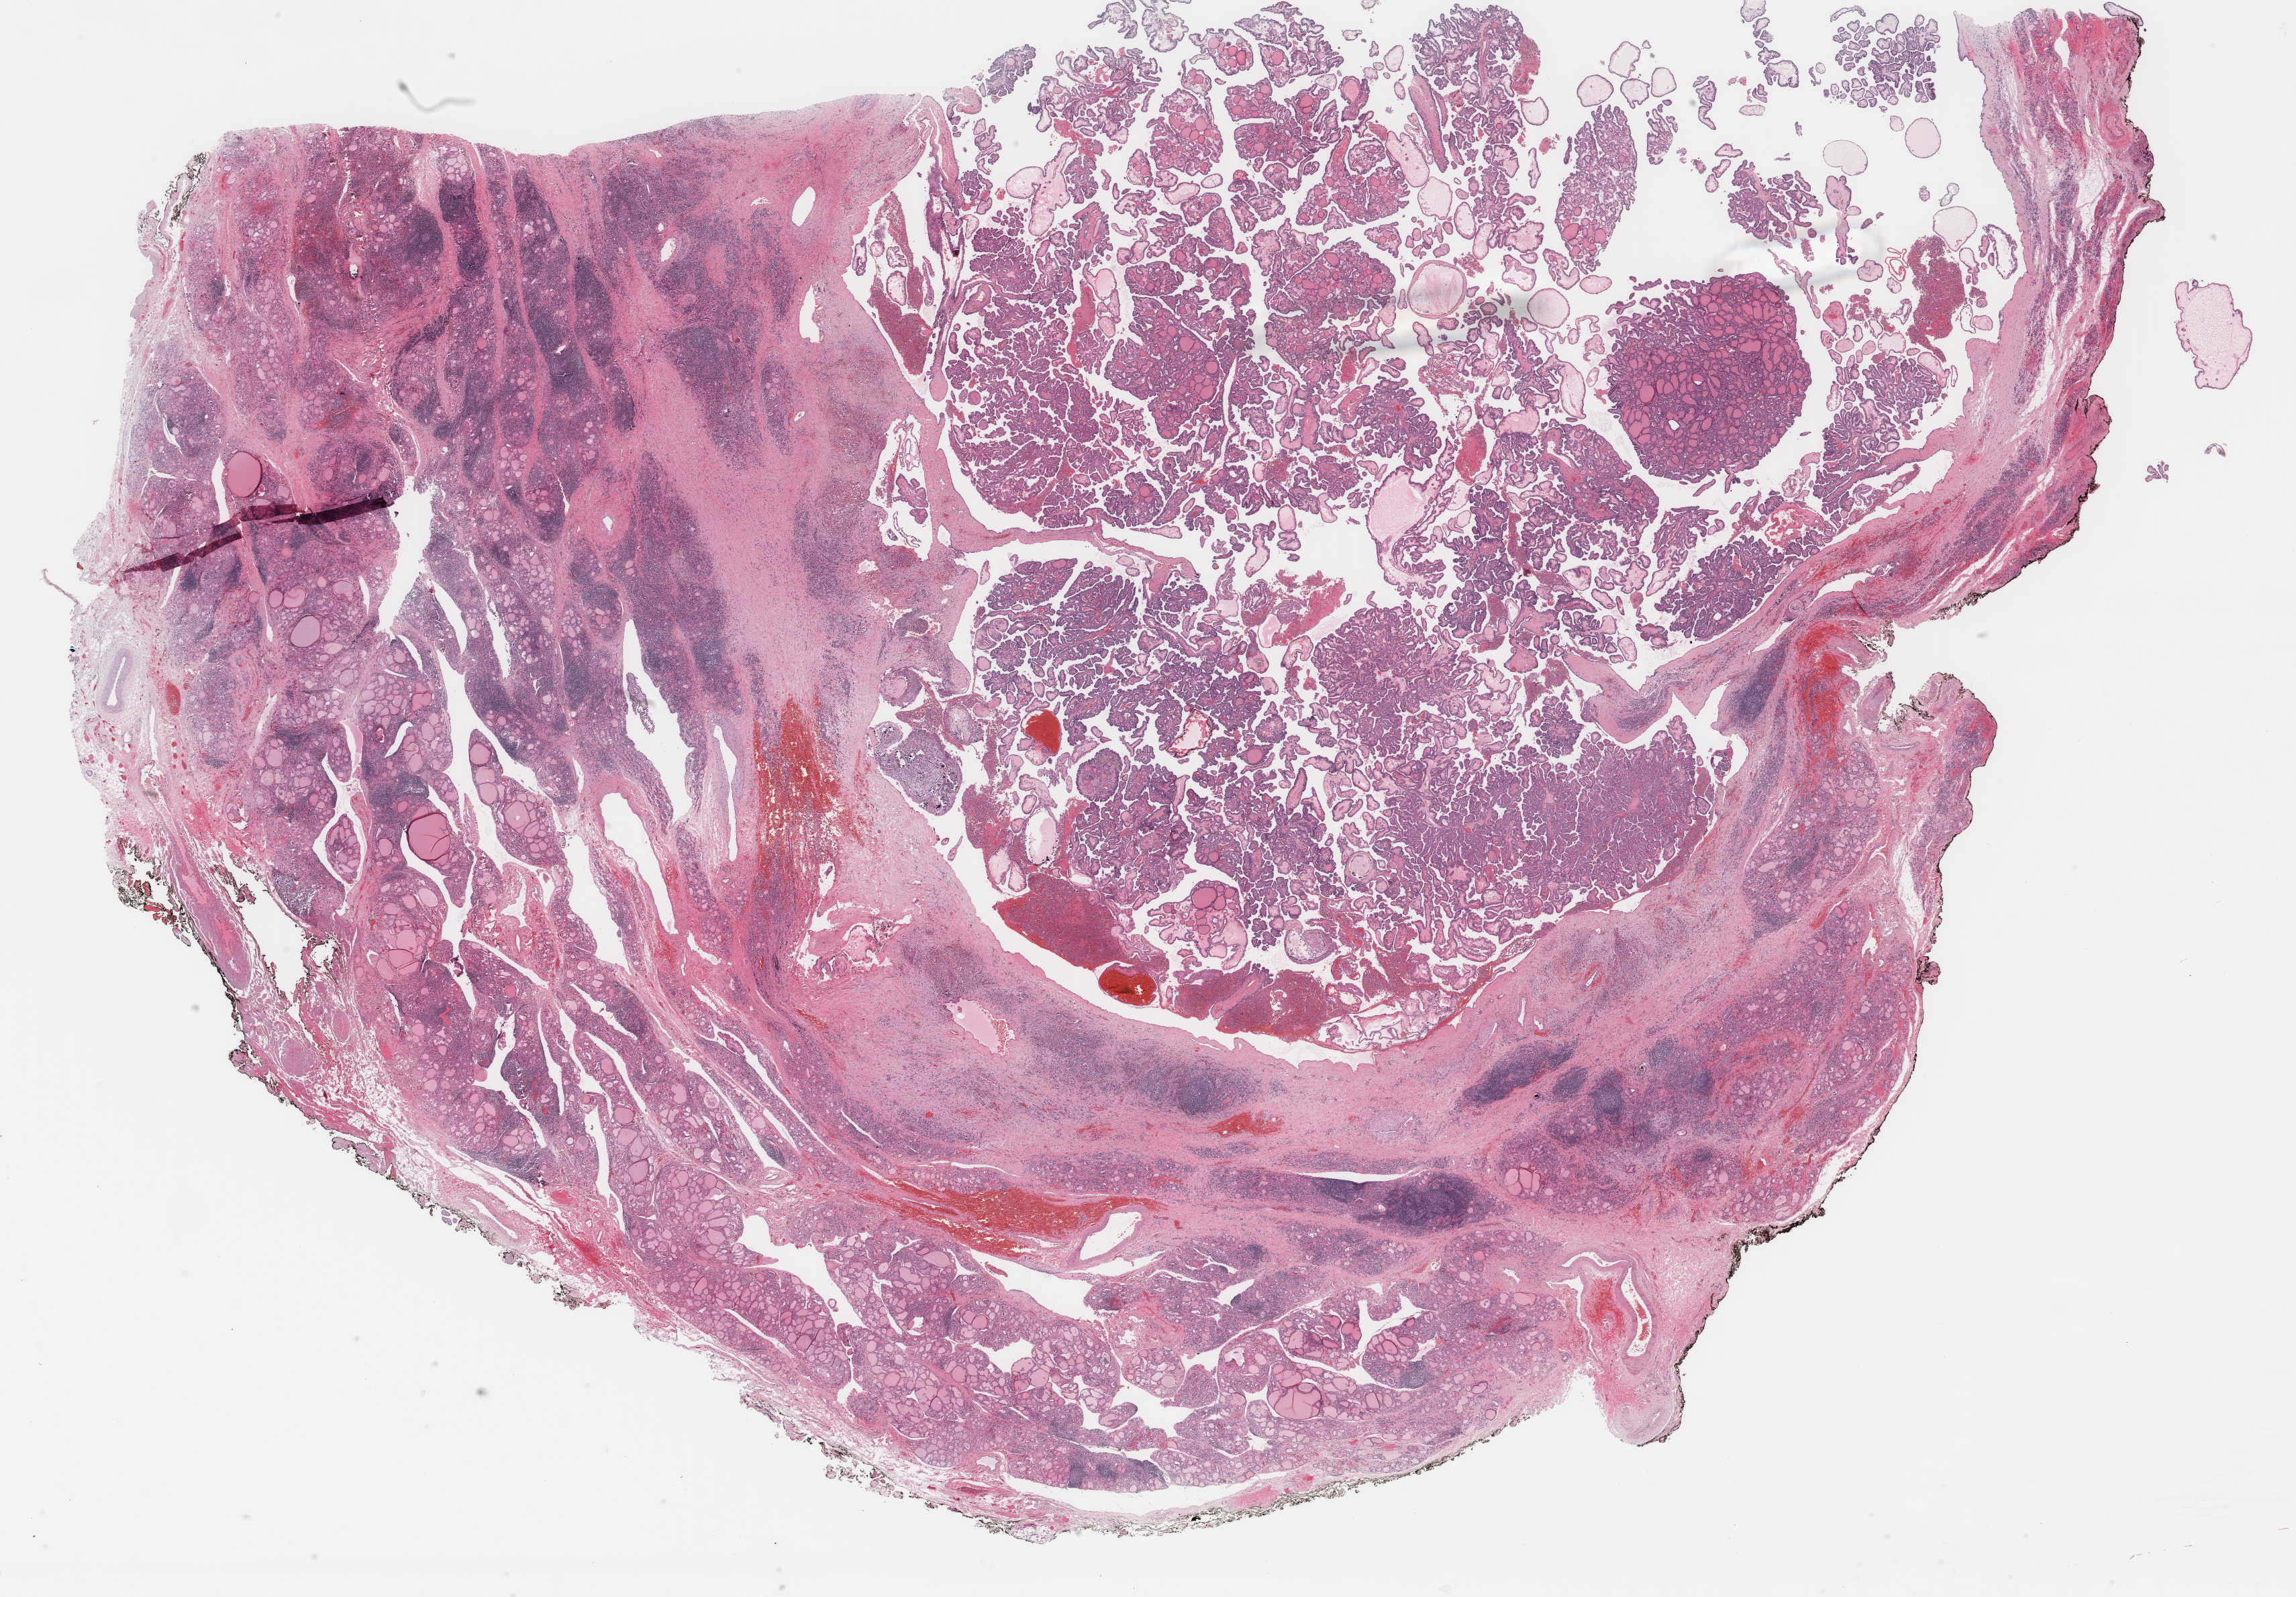
H&E whole-slide image, shown as a low-resolution overview of the whole scanned area (about 27.2 x 18.9 mm, slide scanned at 40x); FFPE section; thyroid, primary tumour sample. Female, age 37 years at initial diagnosis.
AJCC pathologic stage: I (6th edition). Diagnosis: Papillary adenocarcinoma, NOS. TNM: T3 N1 MX. Laterality: left.